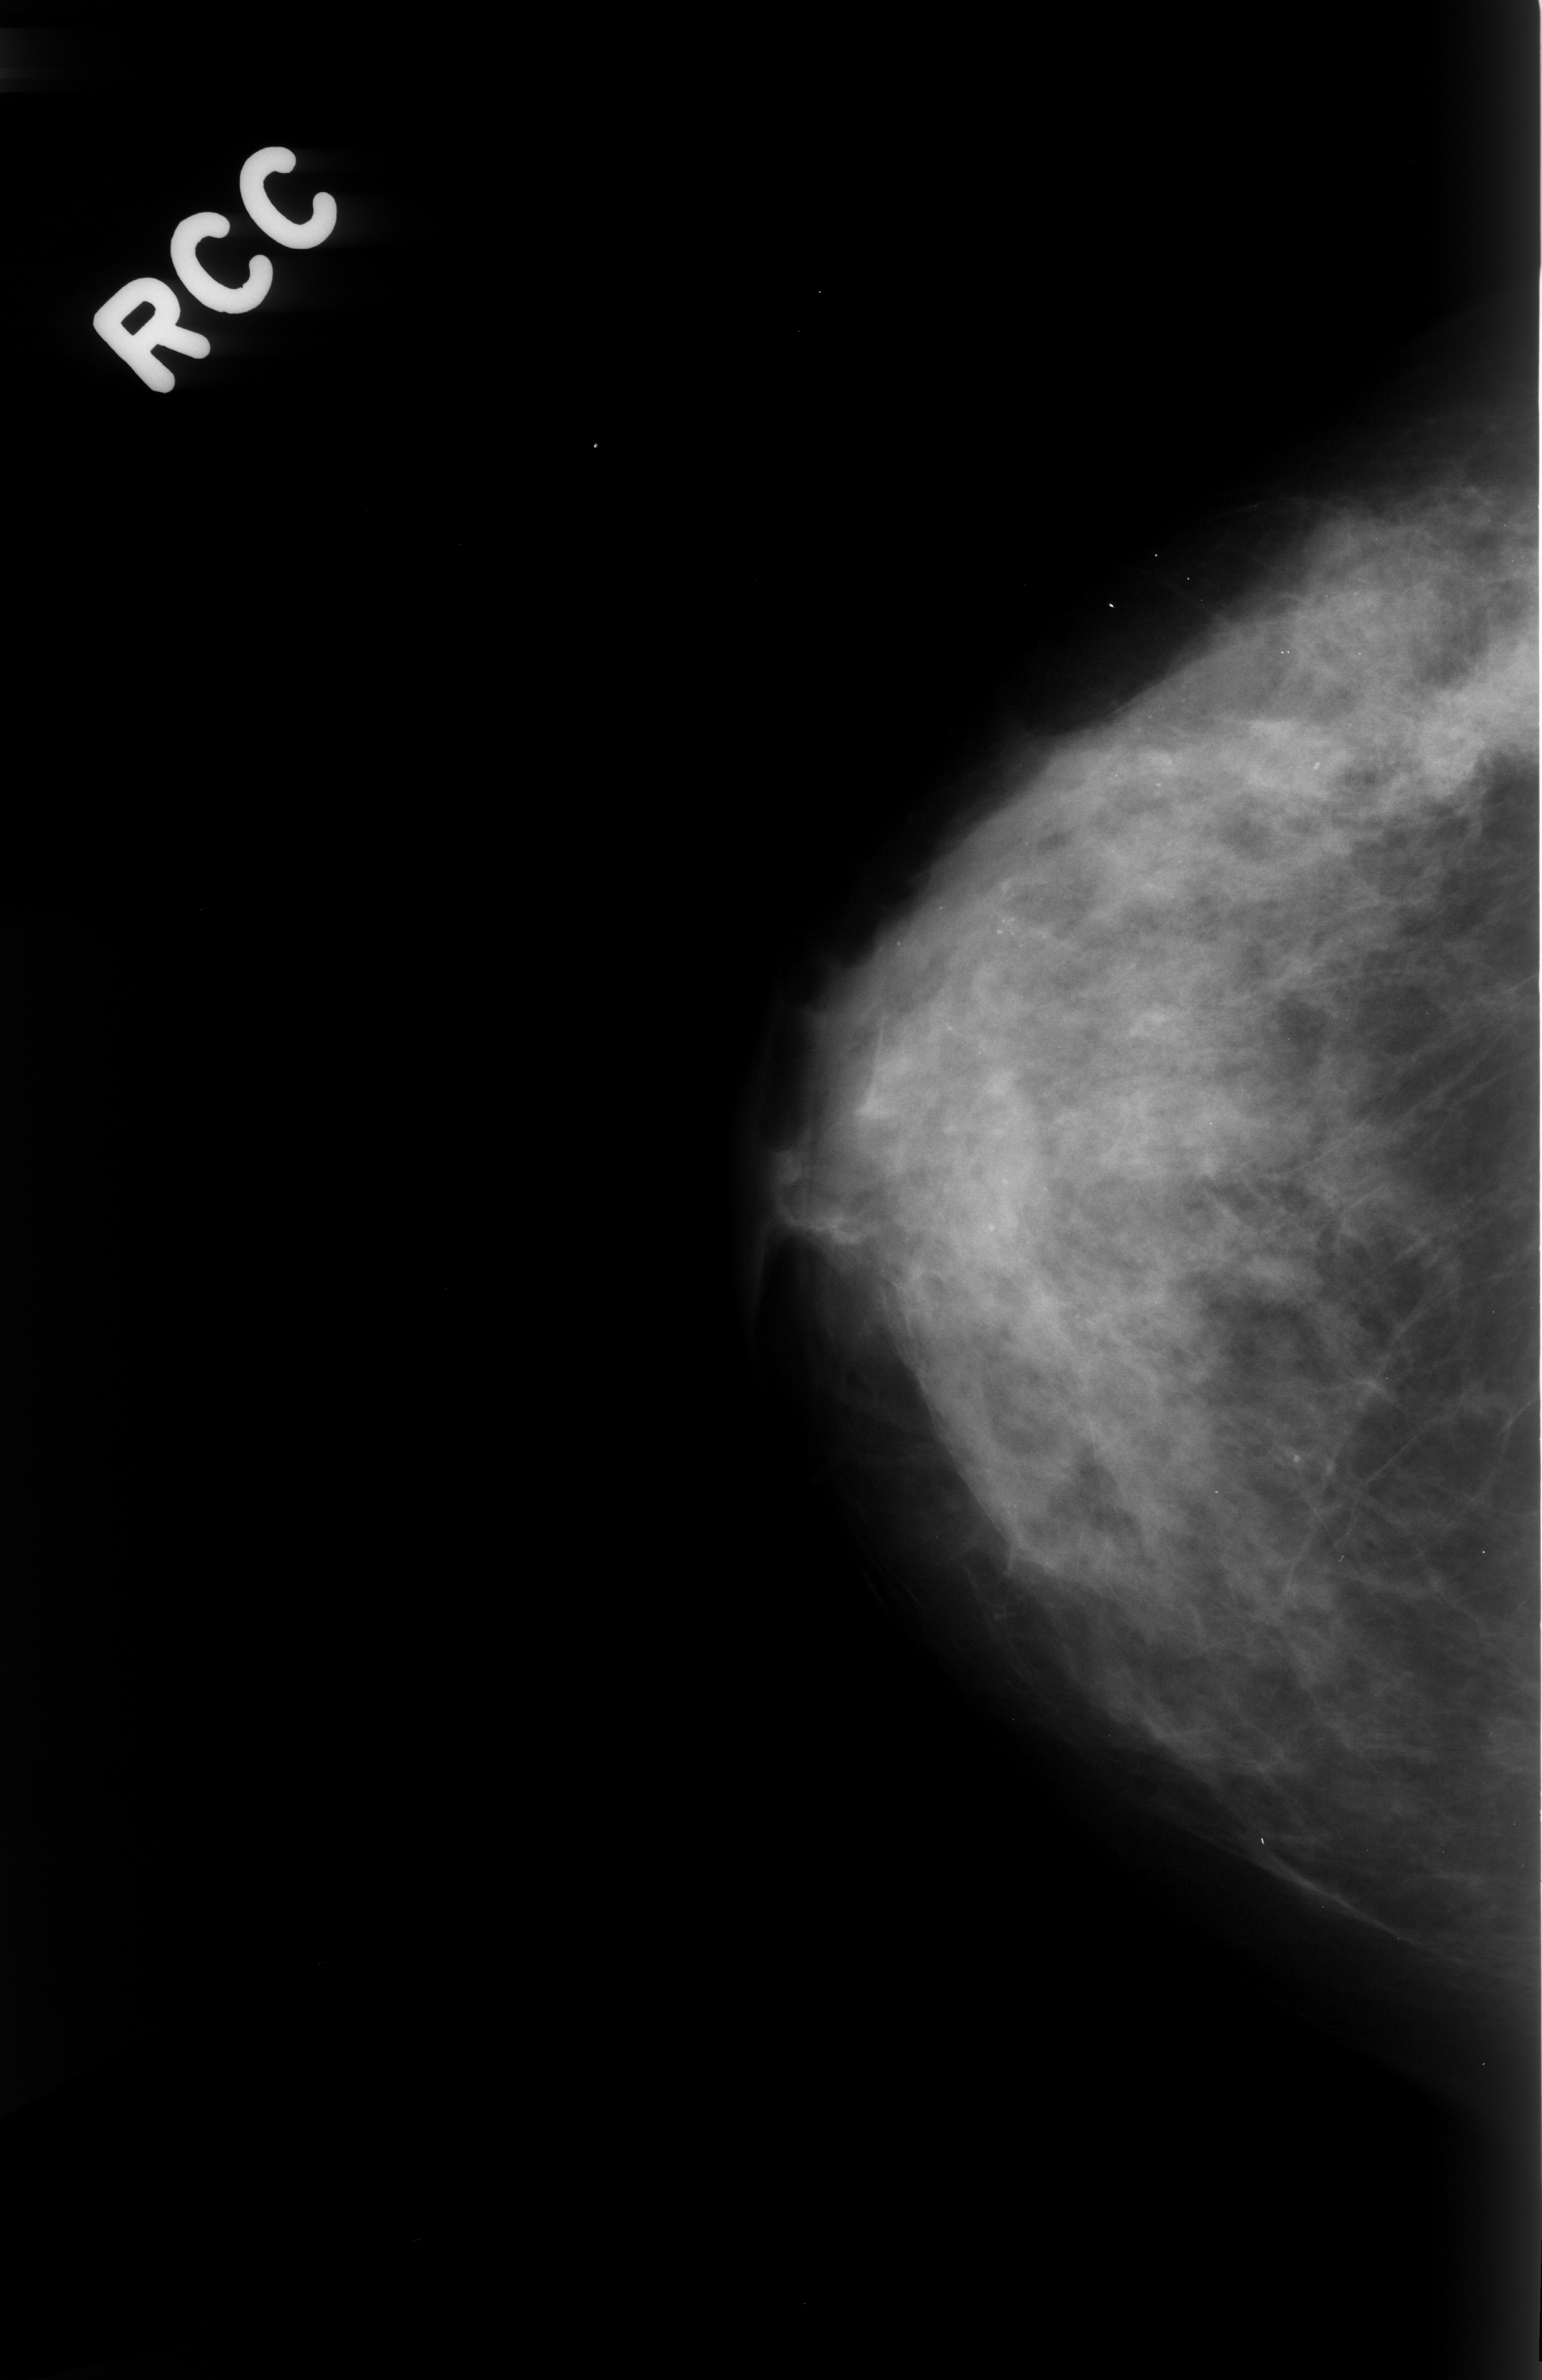
Mammogram (digitized film); right breast; craniocaudal (CC) view; 1542 × 2380 image matrix.
Expert-marked regions of interest on this film, with their recorded descriptors:
- calcifications, morphology pleomorphic, distribution diffusely scattered; BI-RADS assessment category 3; pathology (as recorded): benign: box from (x=788, y=542) to (x=1539, y=1978) px